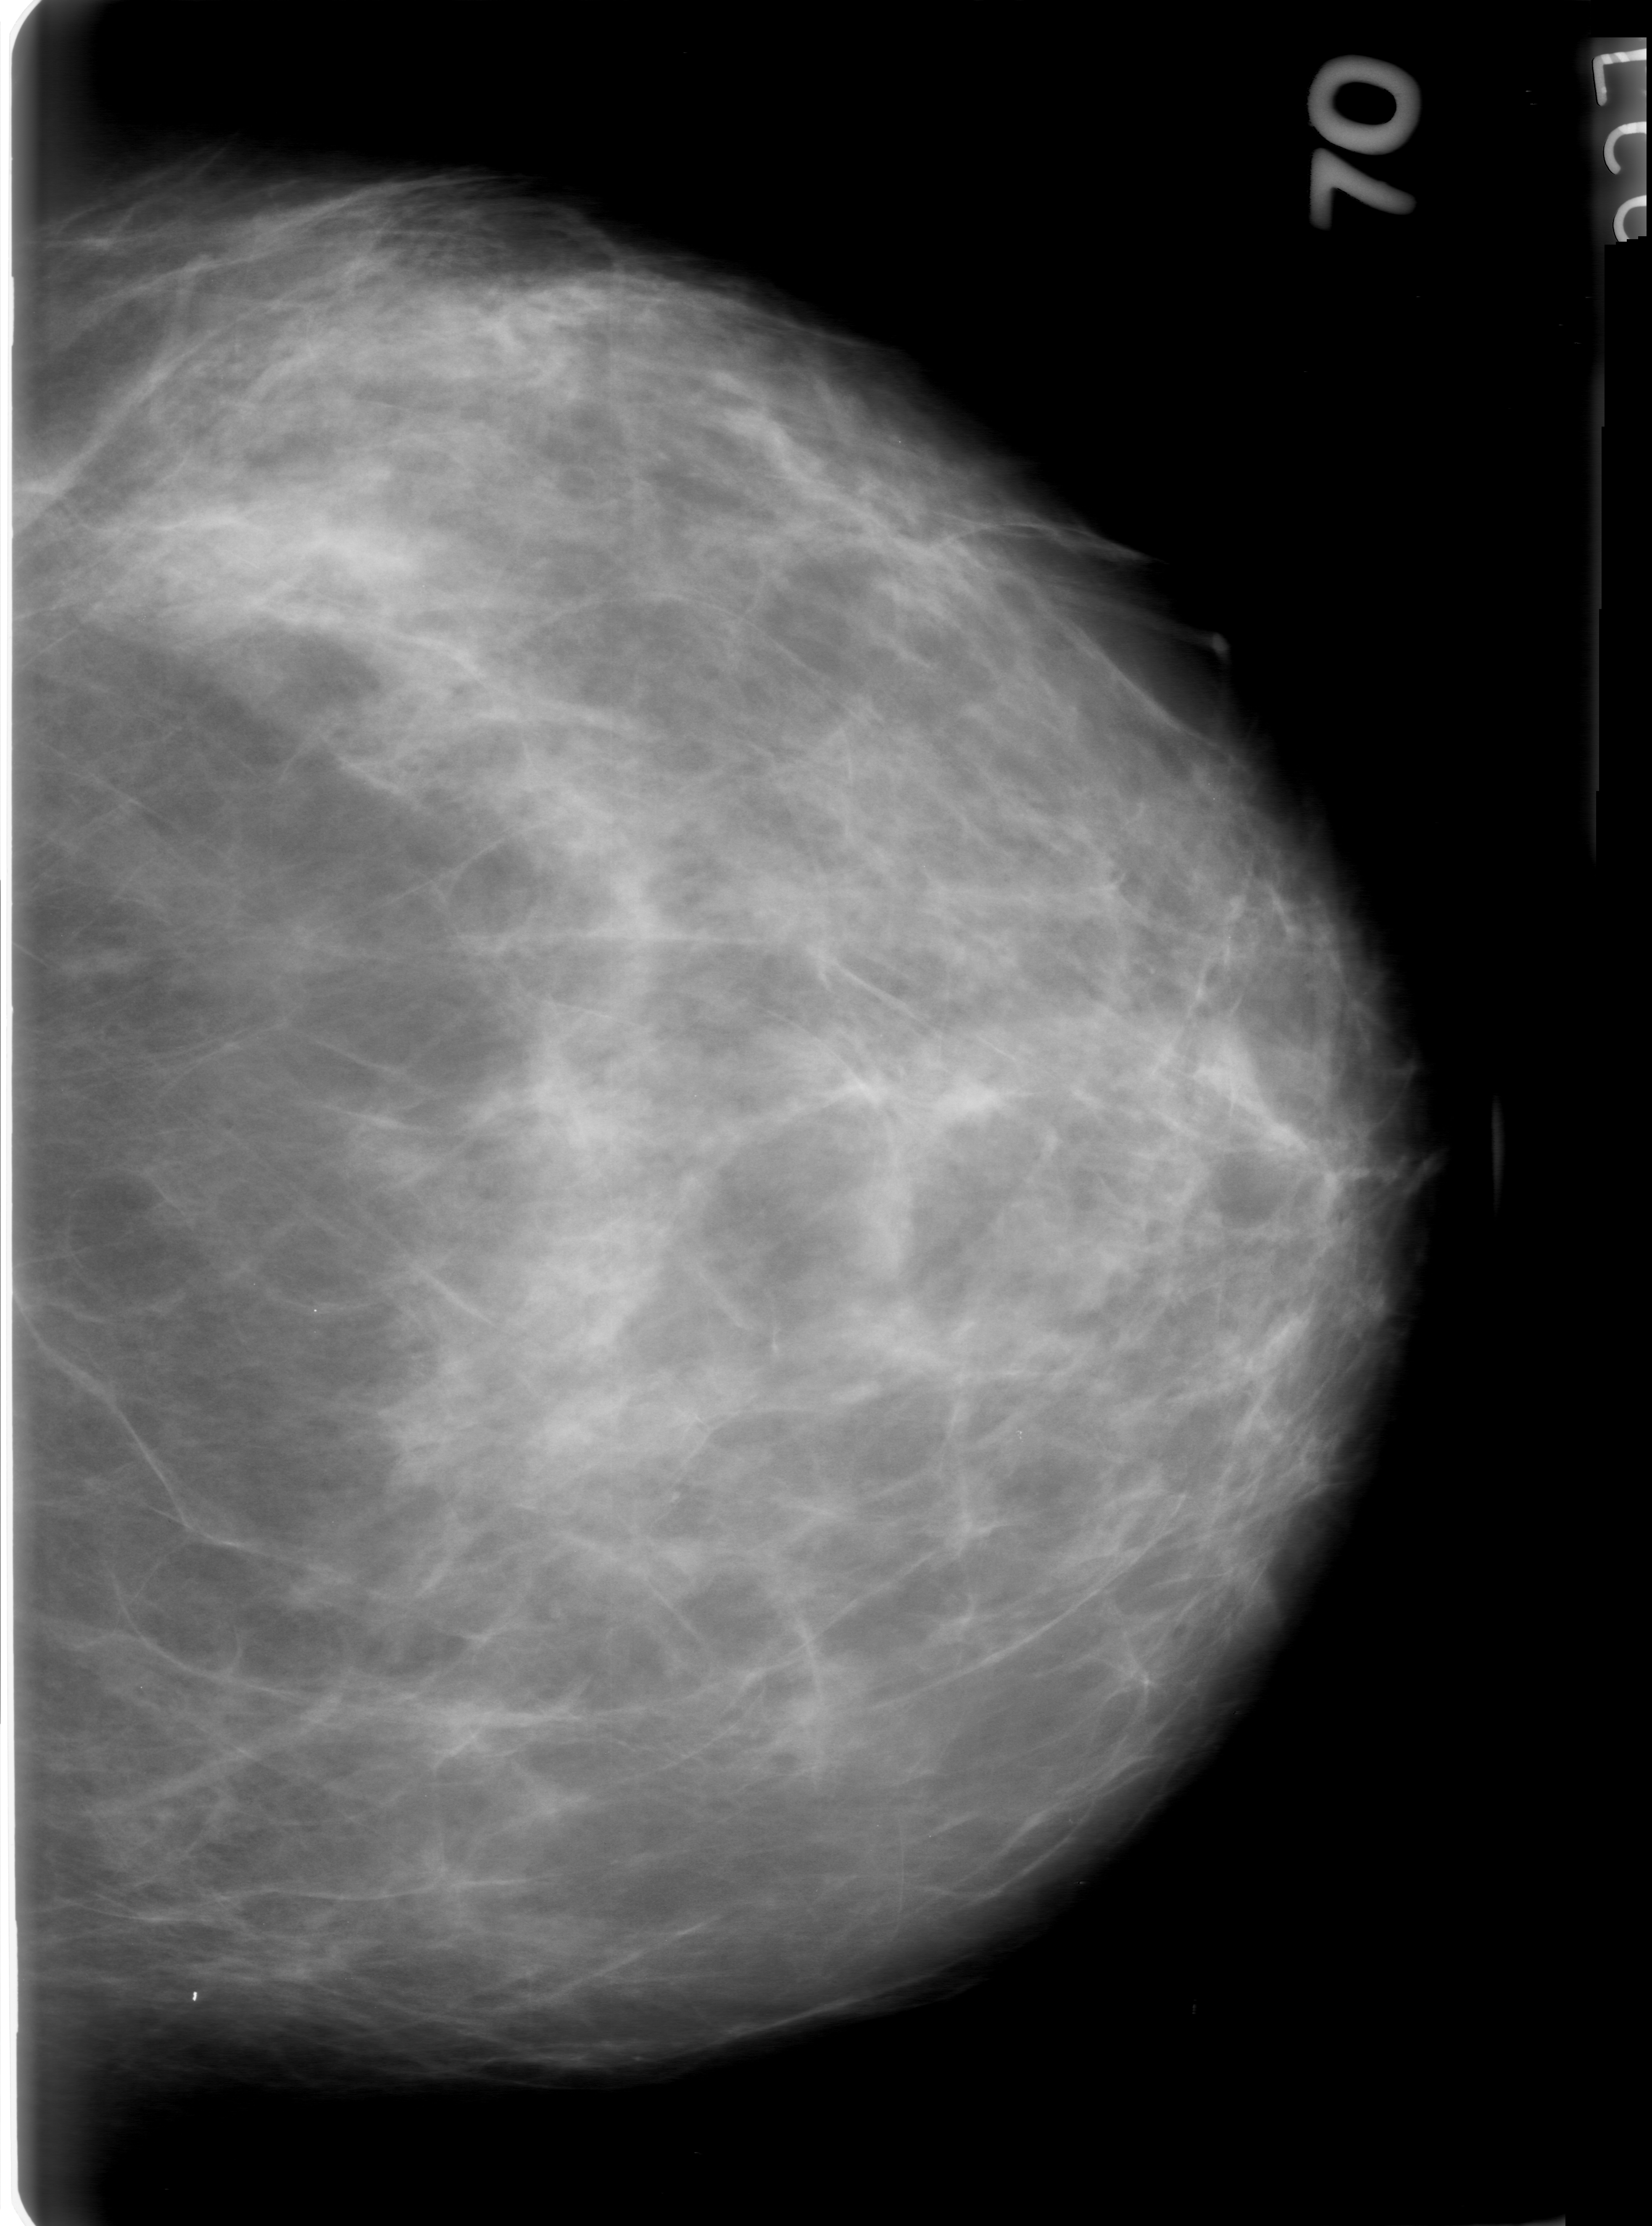
Digitized screen-film mammogram, left breast, CC view, breast composition: heterogeneously dense (BI-RADS density category 3 of 4).
- Marked findings (only marked abnormalities are described; nothing is implied about the rest of the image): mass, shape oval, margins obscured; BI-RADS assessment category 0; pathology result (as recorded, not read from the image): benign.